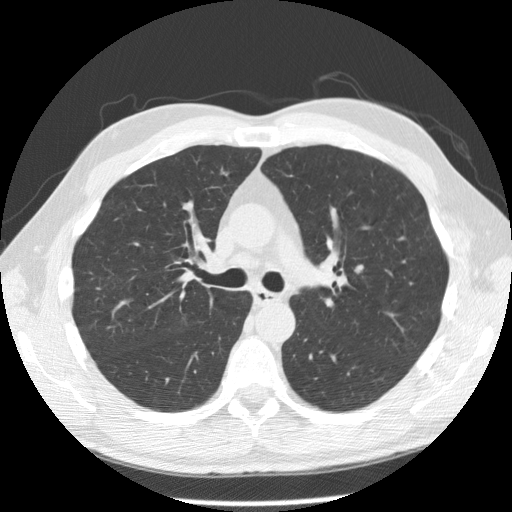
Chest CT (low-dose screening protocol), one axial image. Second screening round (one year after baseline). Lung window (W 1500 / L -600 HU). Slice 121 of 181 in the series. Male participant, aged 55 years at enrolment. Current smoker at enrolment.
• Lesion marked by an expert reader, box from (x=333, y=251) to (x=376, y=294) px.
• Screening reader's record for this exam: no non-calcified nodule ≥4 mm recorded.
• Later outcome: lung cancer diagnosed 356 days after this screen — small cell carcinoma, NOS, left upper lobe, undifferentiated (G4), stage IV (AJCC 6th edition), 60 mm at pathology.